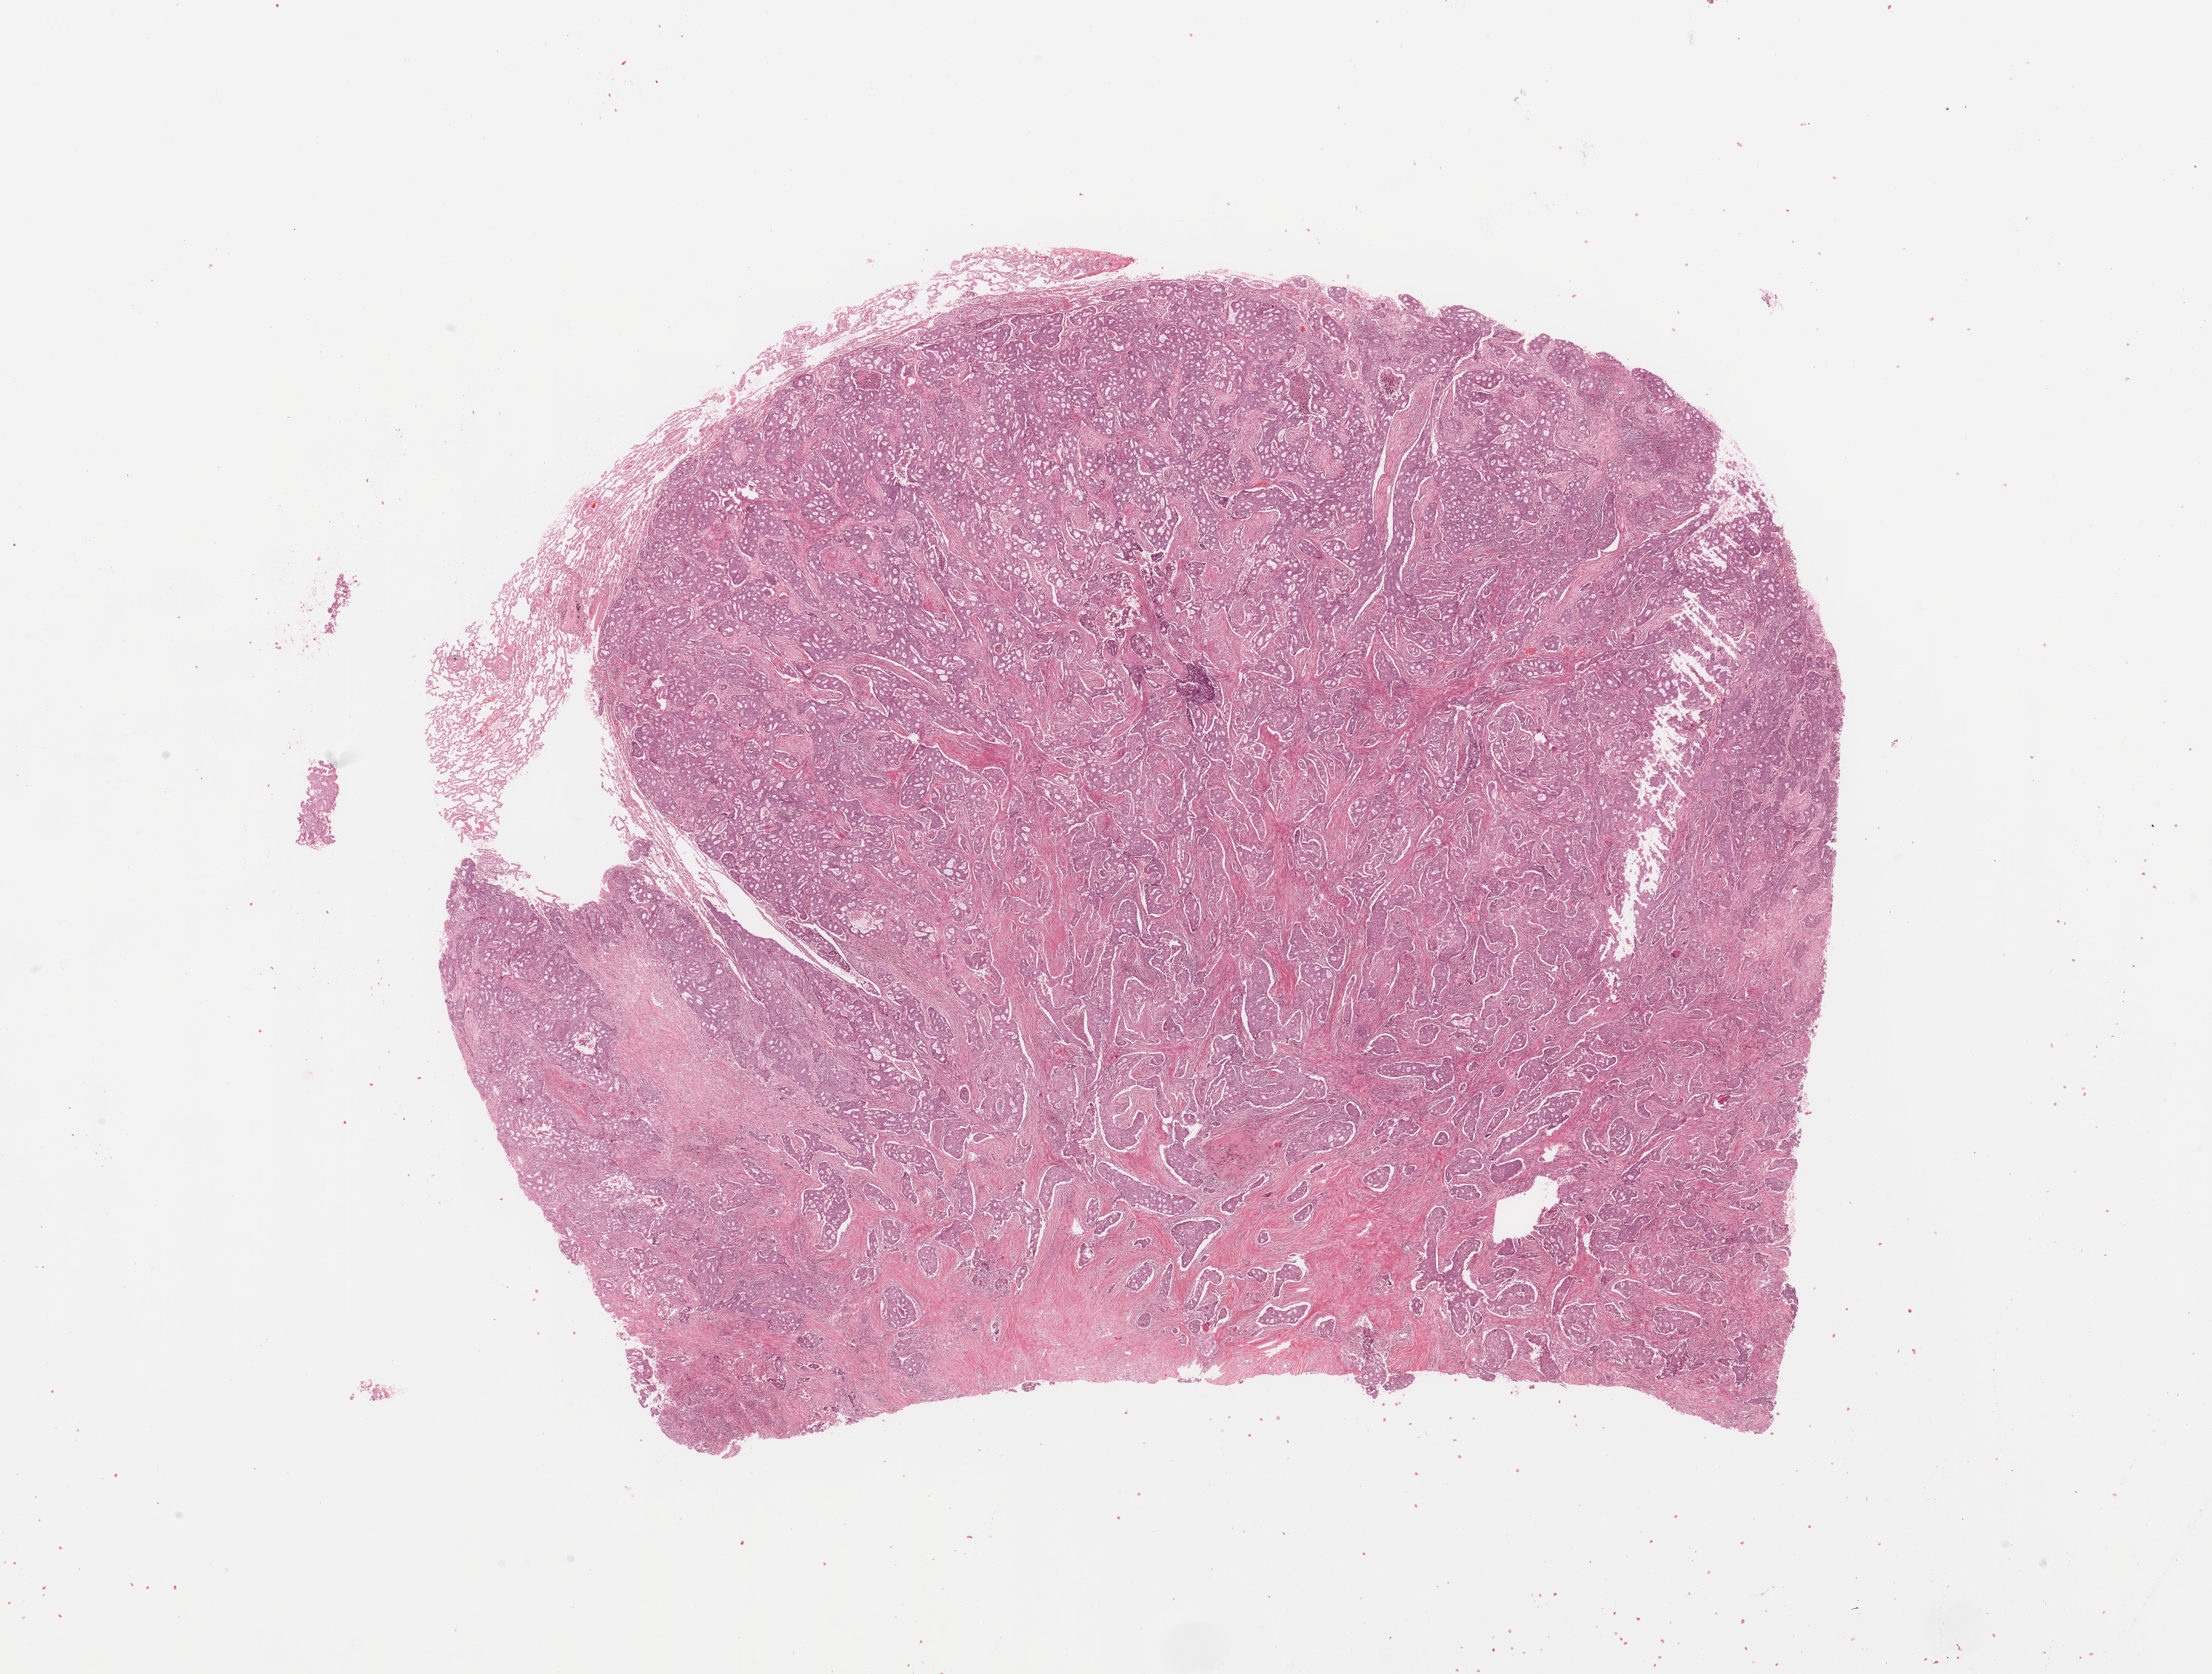
H&E-stained whole-slide image — shown as a low-resolution overview of the whole scanned area (about 23.6 x 17.9 mm, from a 20x scan), tumour tissue sample, sampled site: lung. 67-year-old male patient. Histologic grade: G2 (moderately differentiated). Composition of this section per pathologist review: tumour nuclei 75%, necrosis 5%.
AJCC pathologic stage: IB. Diagnosis: Adenocarcinoma, NOS.